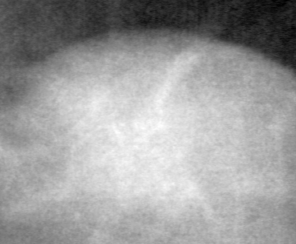
Crop from a digitized film mammogram around one marked abnormality, right breast, CC view, BI-RADS breast density category 1 (scale 1–4).
Finding: mass, shape oval, margins obscured; BI-RADS assessment category 4; pathology result (as recorded, not read from the image): benign.